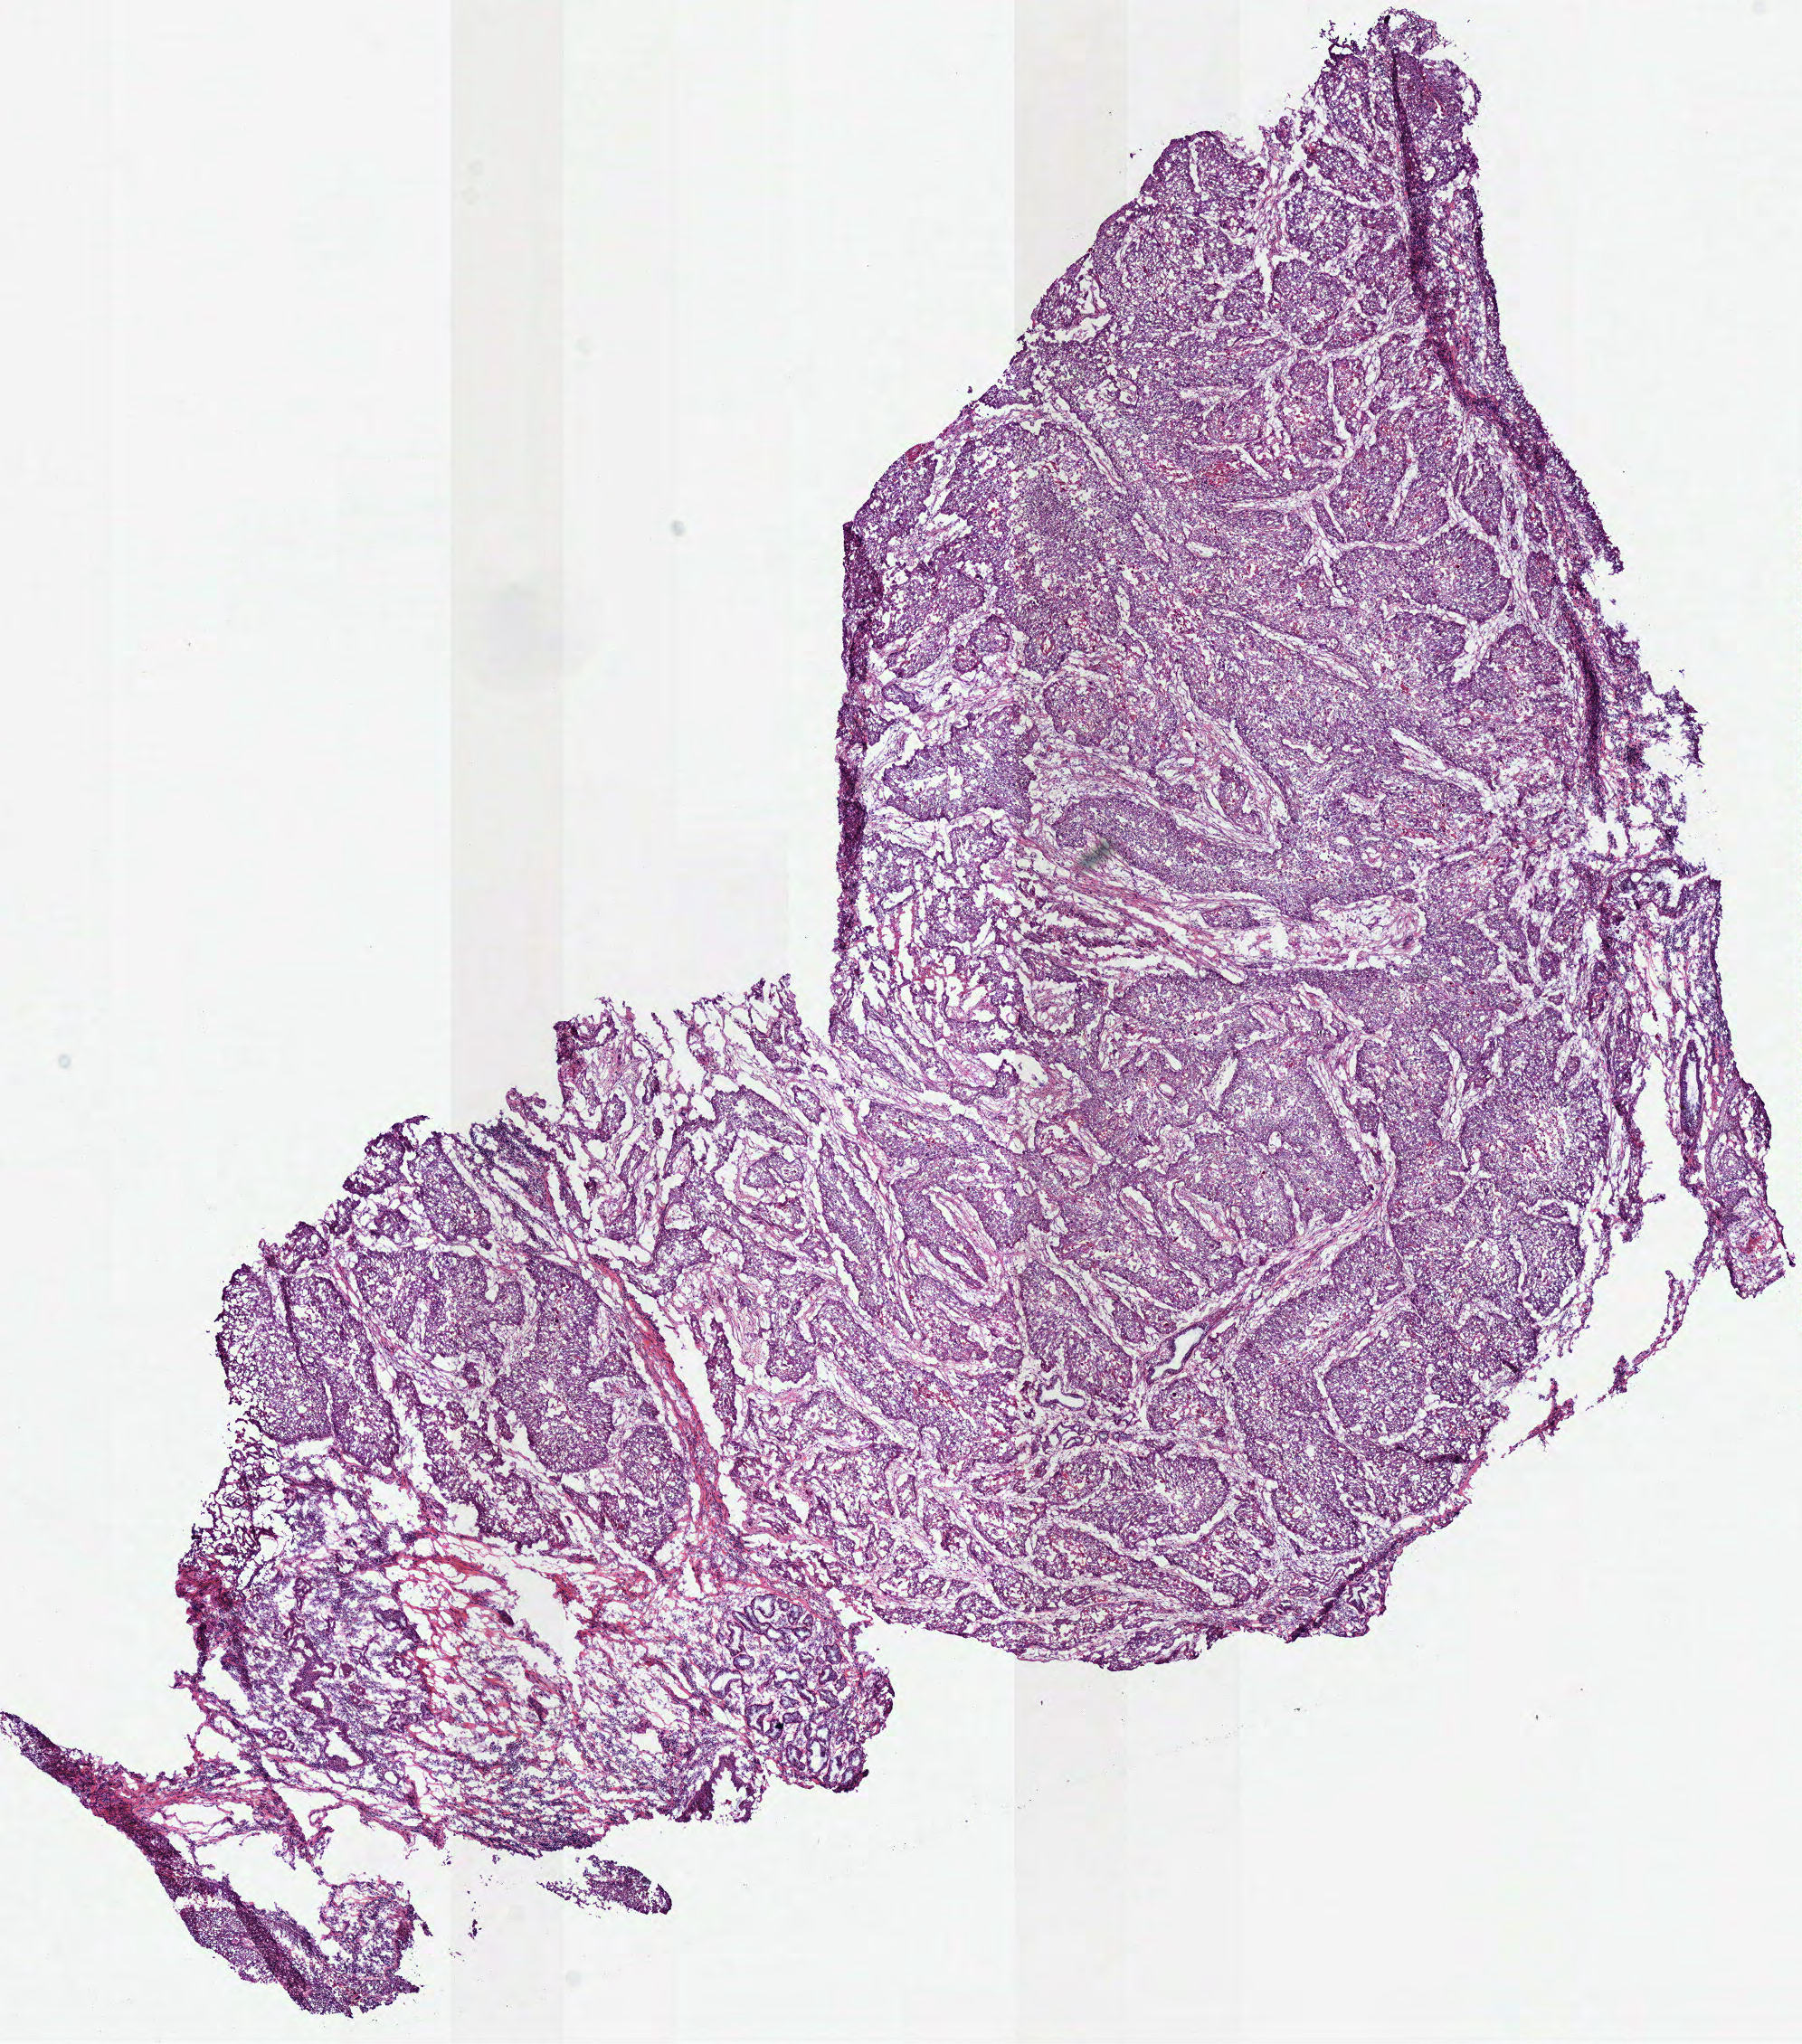
H&E-stained whole-slide image, low-resolution overview of the scanned area, about 7.8 x 8.9 mm, frozen section, head and neck, primary tumour sample. Male, age 47 years at initial diagnosis. Histologic grade: G3 (poorly differentiated). Composition of this section per pathologist review: tumour cells 90%, tumour nuclei 80%, normal cells 0%, stromal cells 10%, necrosis 0%.
TNM: T4a N2b. AJCC pathologic stage: IVA. Pathologic diagnosis: Squamous cell carcinoma, NOS (larynx, NOS).